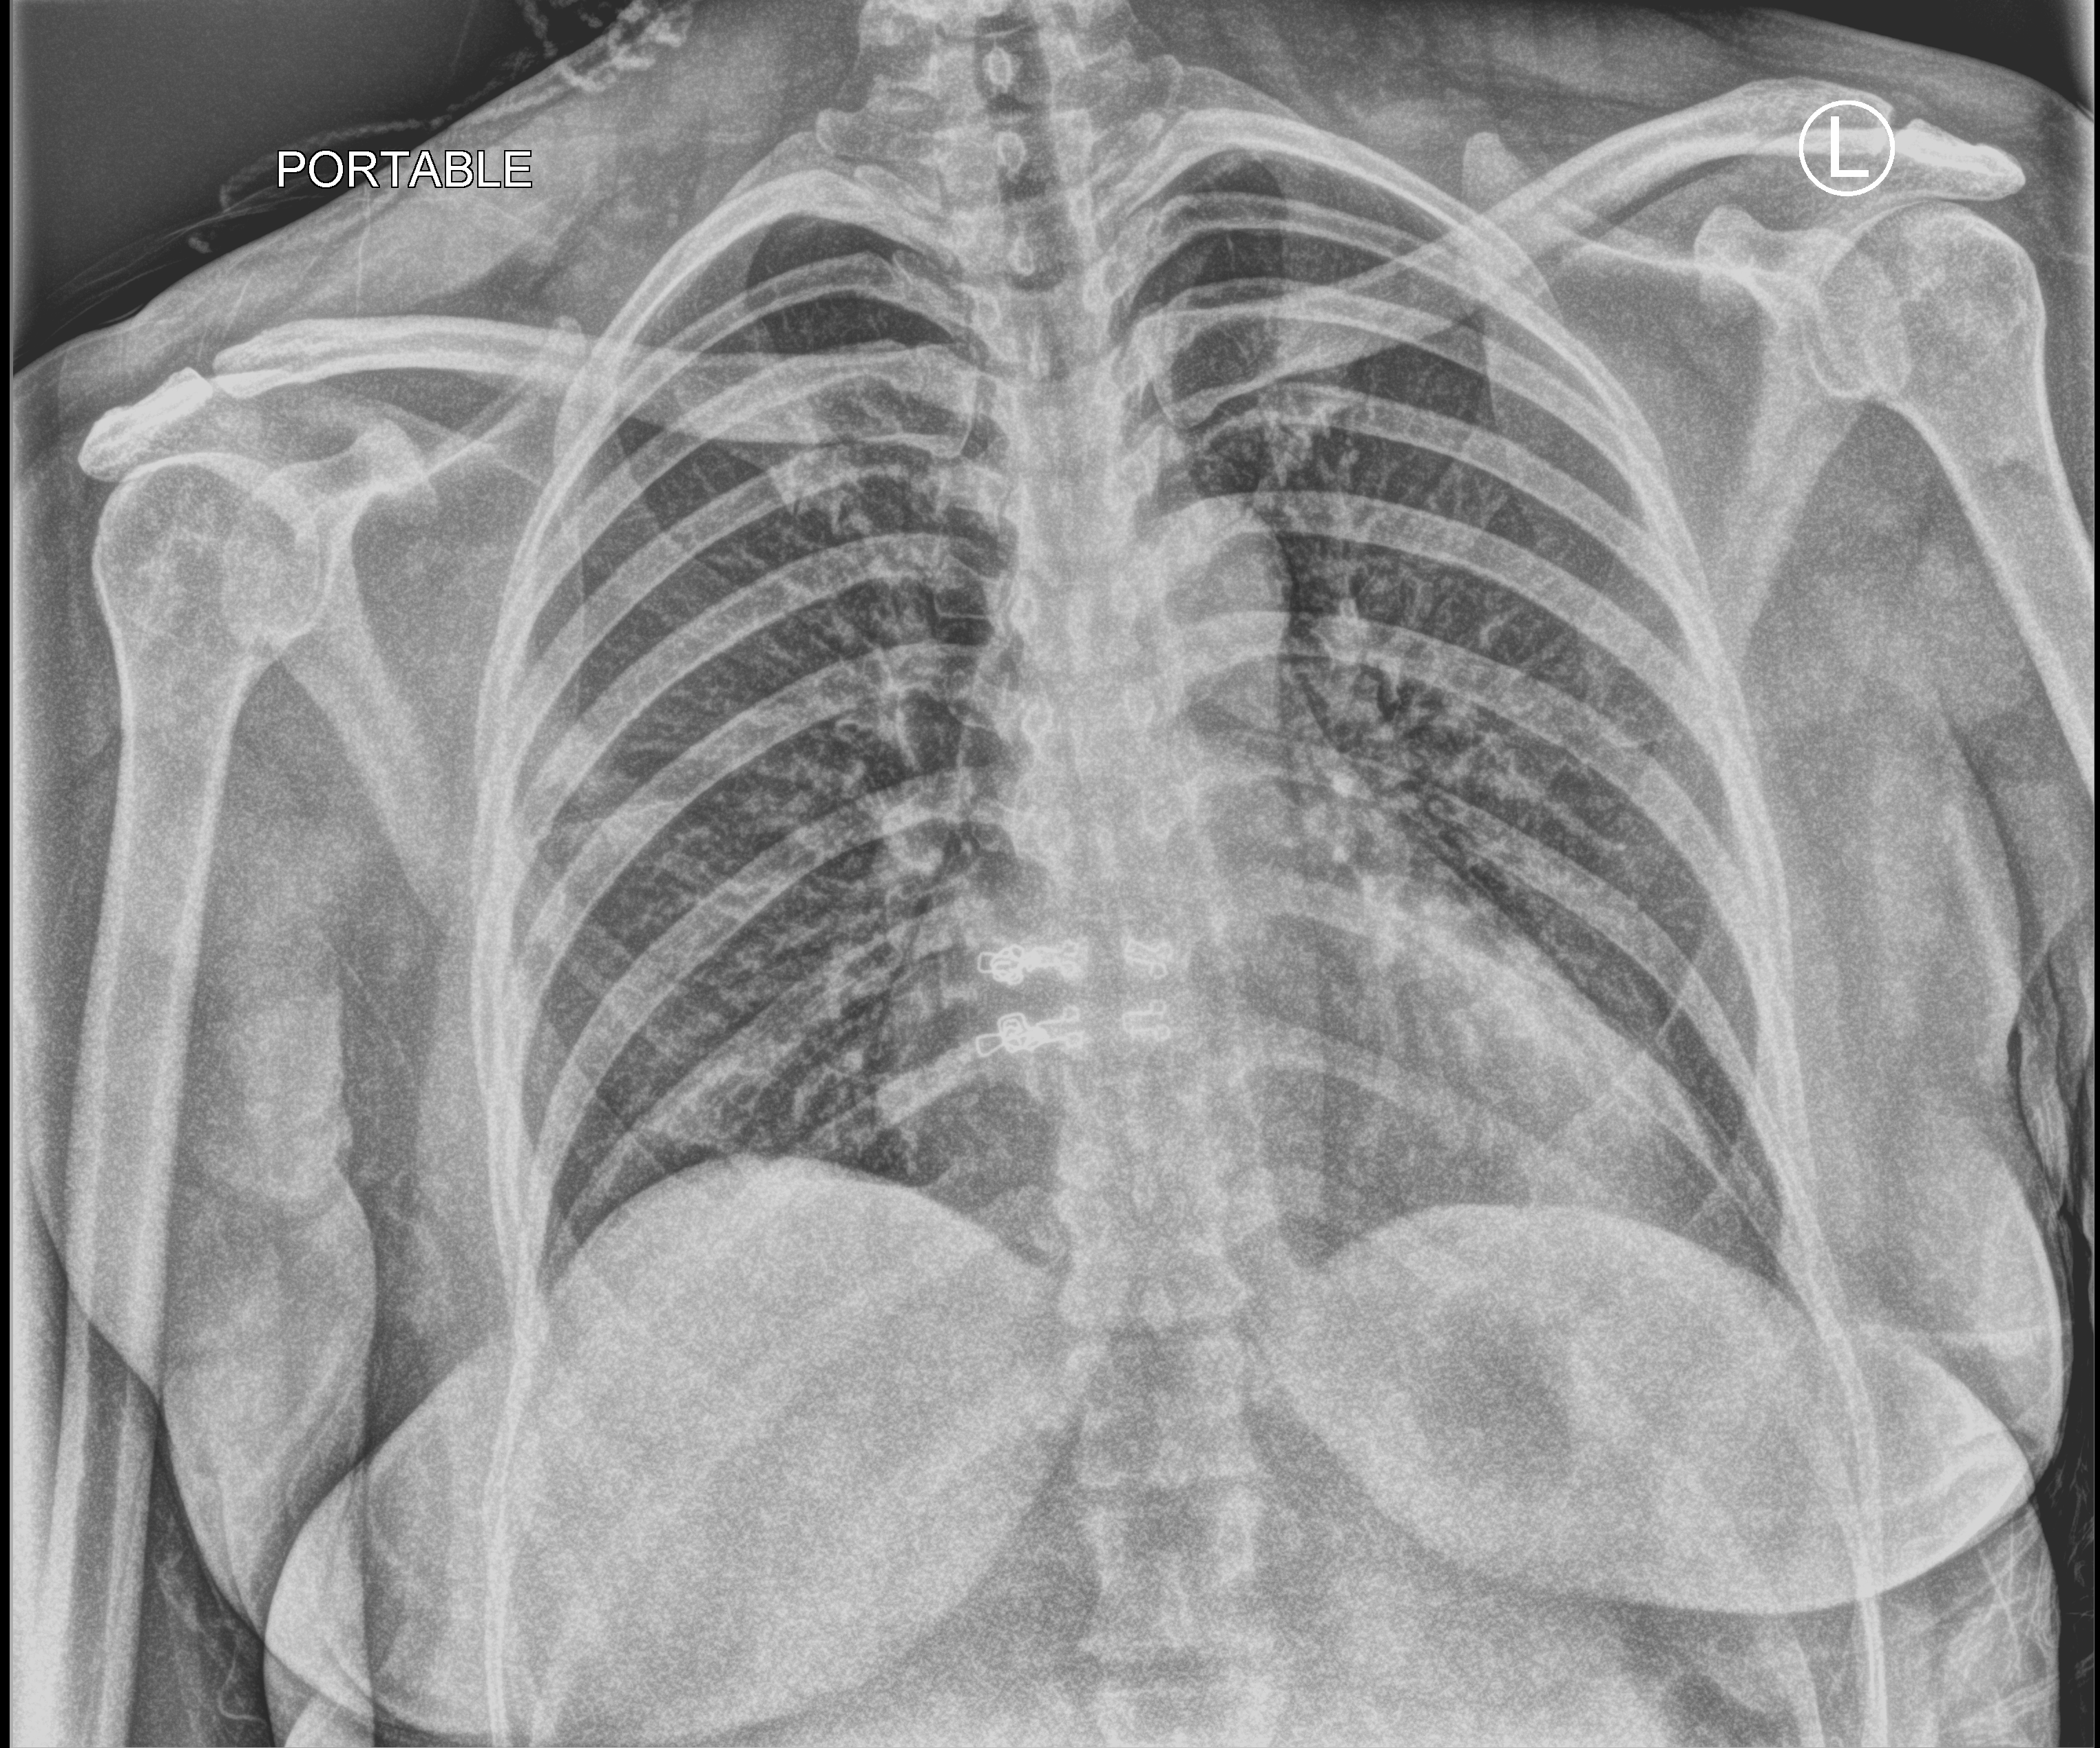
Bedside chest radiograph (computed radiography), anteroposterior (AP) projection. Female patient hospitalised with COVID-19, age 18–59 years.
Hospital-stay facts (about this admission, not read from this image; timing relative to this image not recorded):
- admitted to intensive care during this hospital stay: no